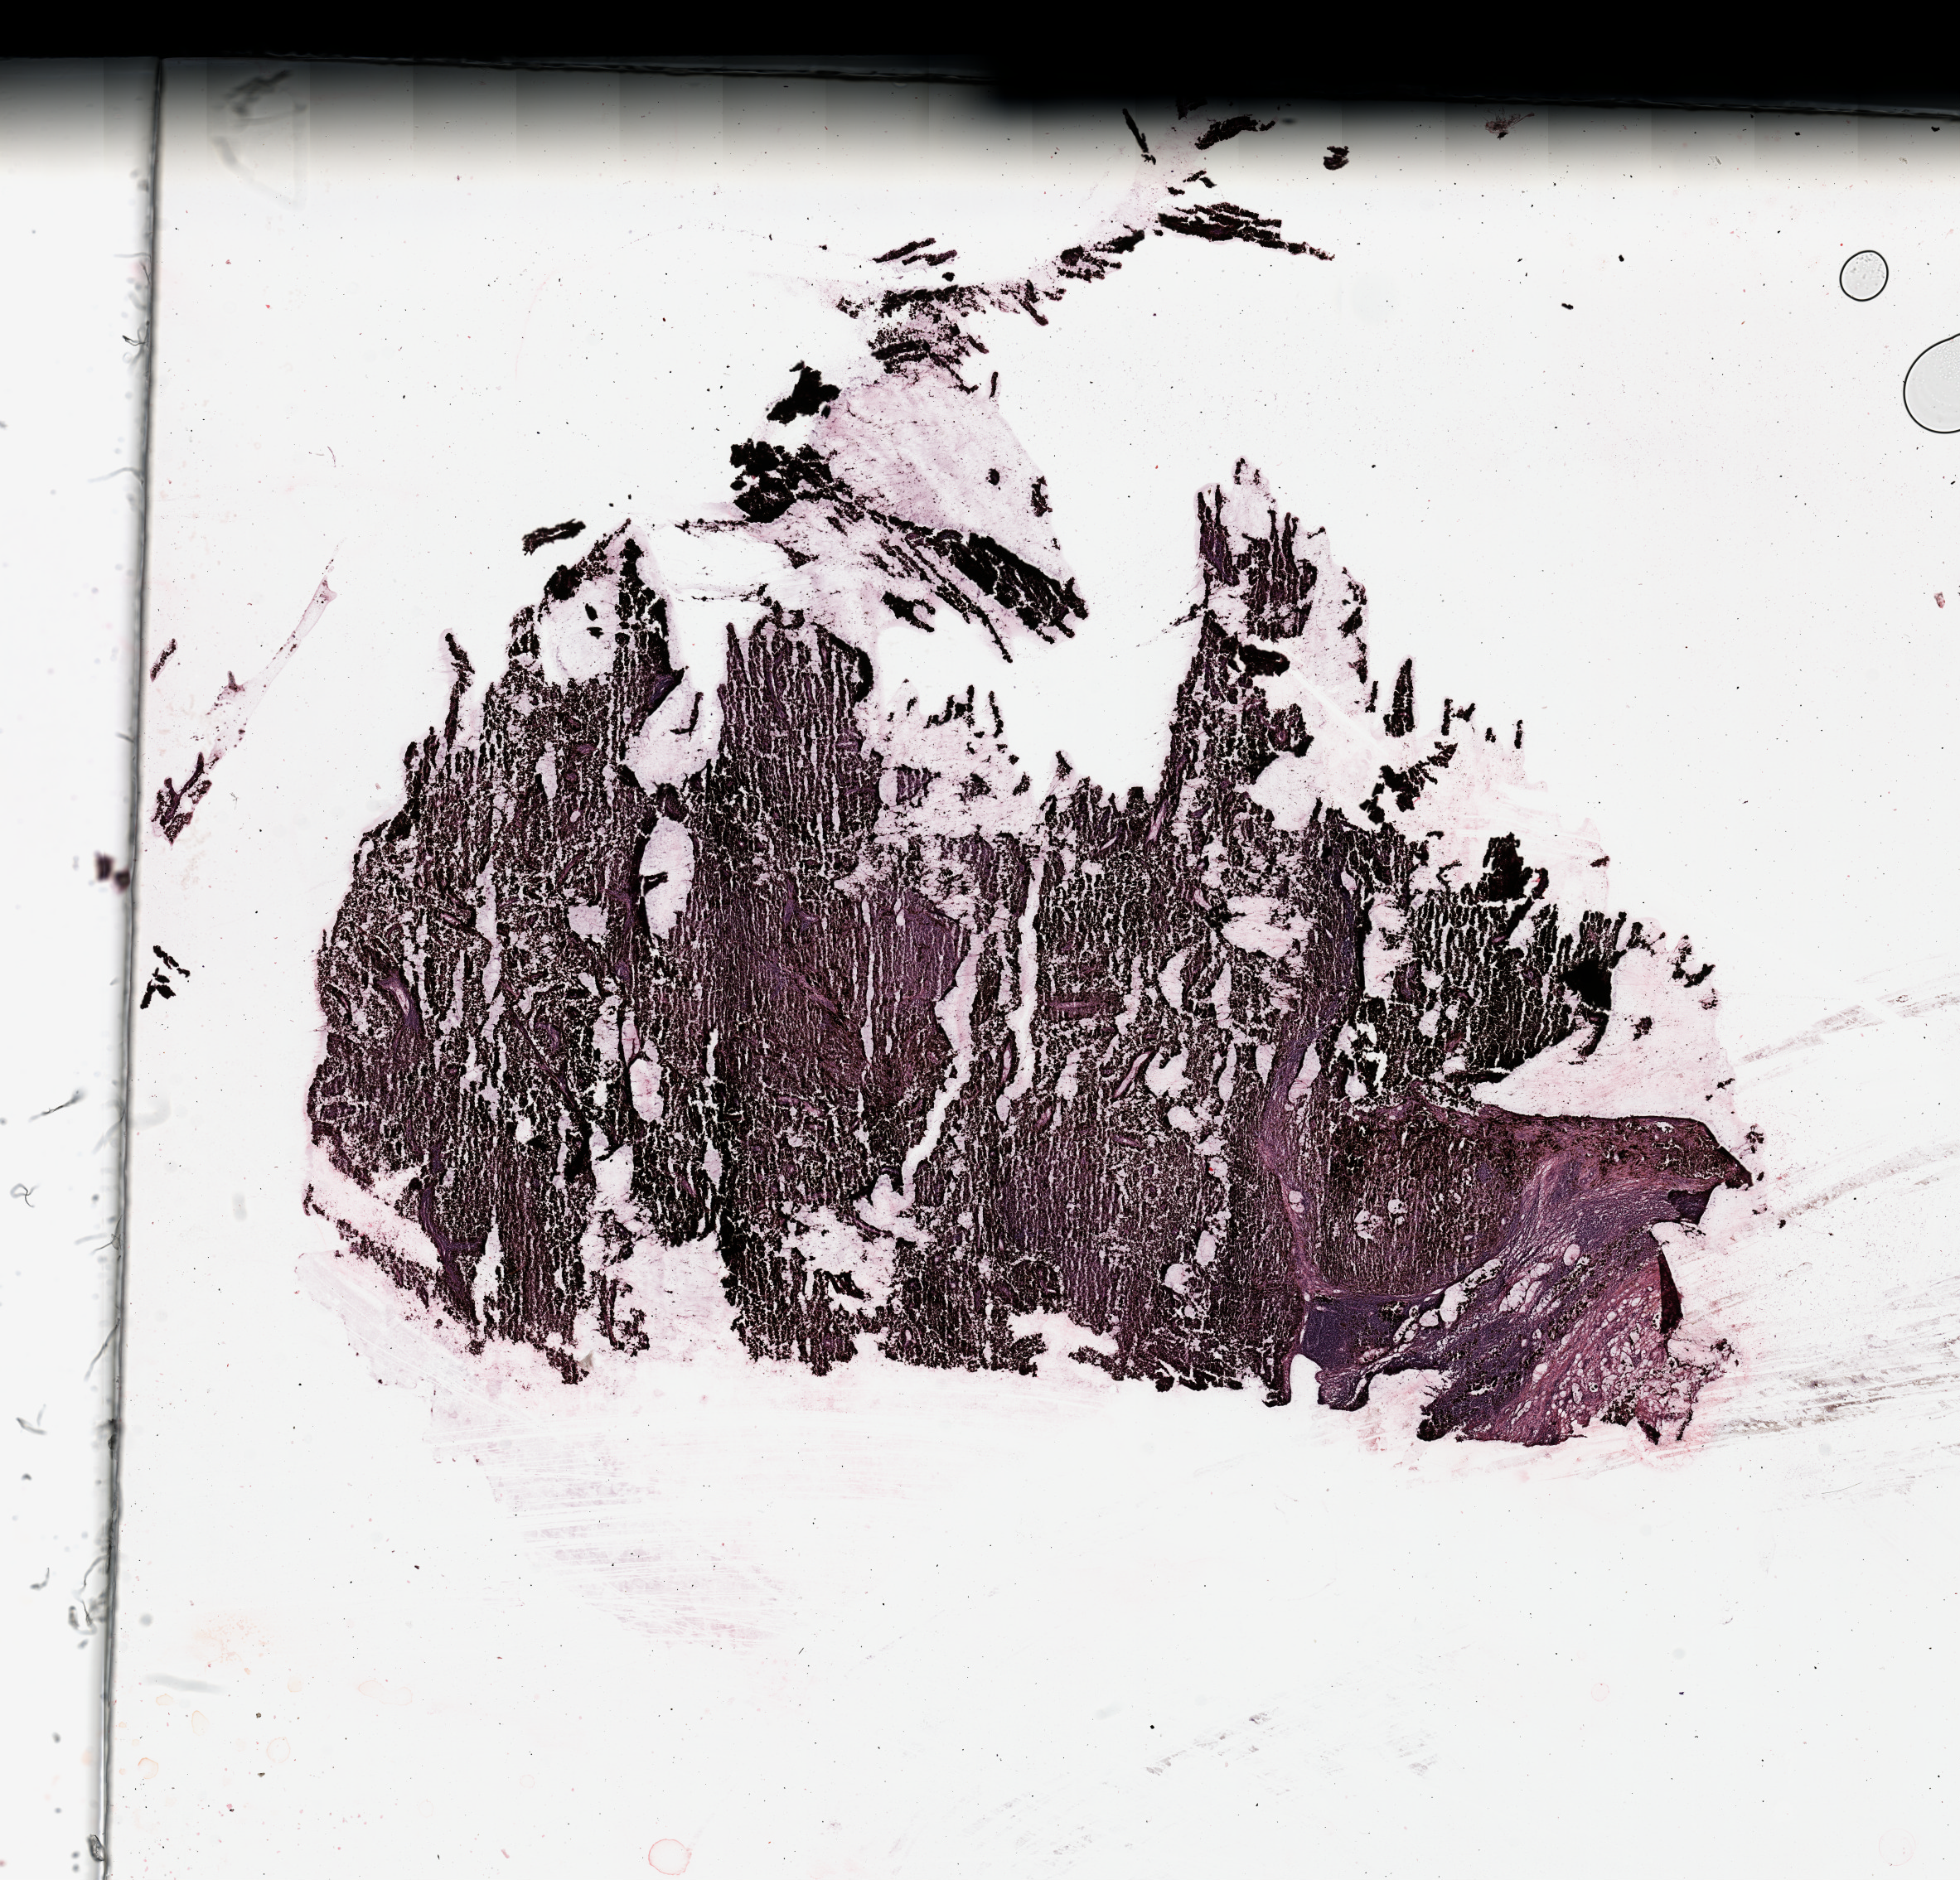
Whole-slide histology image, Hematoxylin and eosin (H&E) stained — whole scanned area (about 18.7 x 17.9 mm) shown as a low-resolution overview, melanoma tumour tissue; sampled site not recorded. 74-year-old female patient.
Primary tumour site (as recorded): trunk. Patient diagnosis (cohort enrolment): cutaneous melanoma (skin).